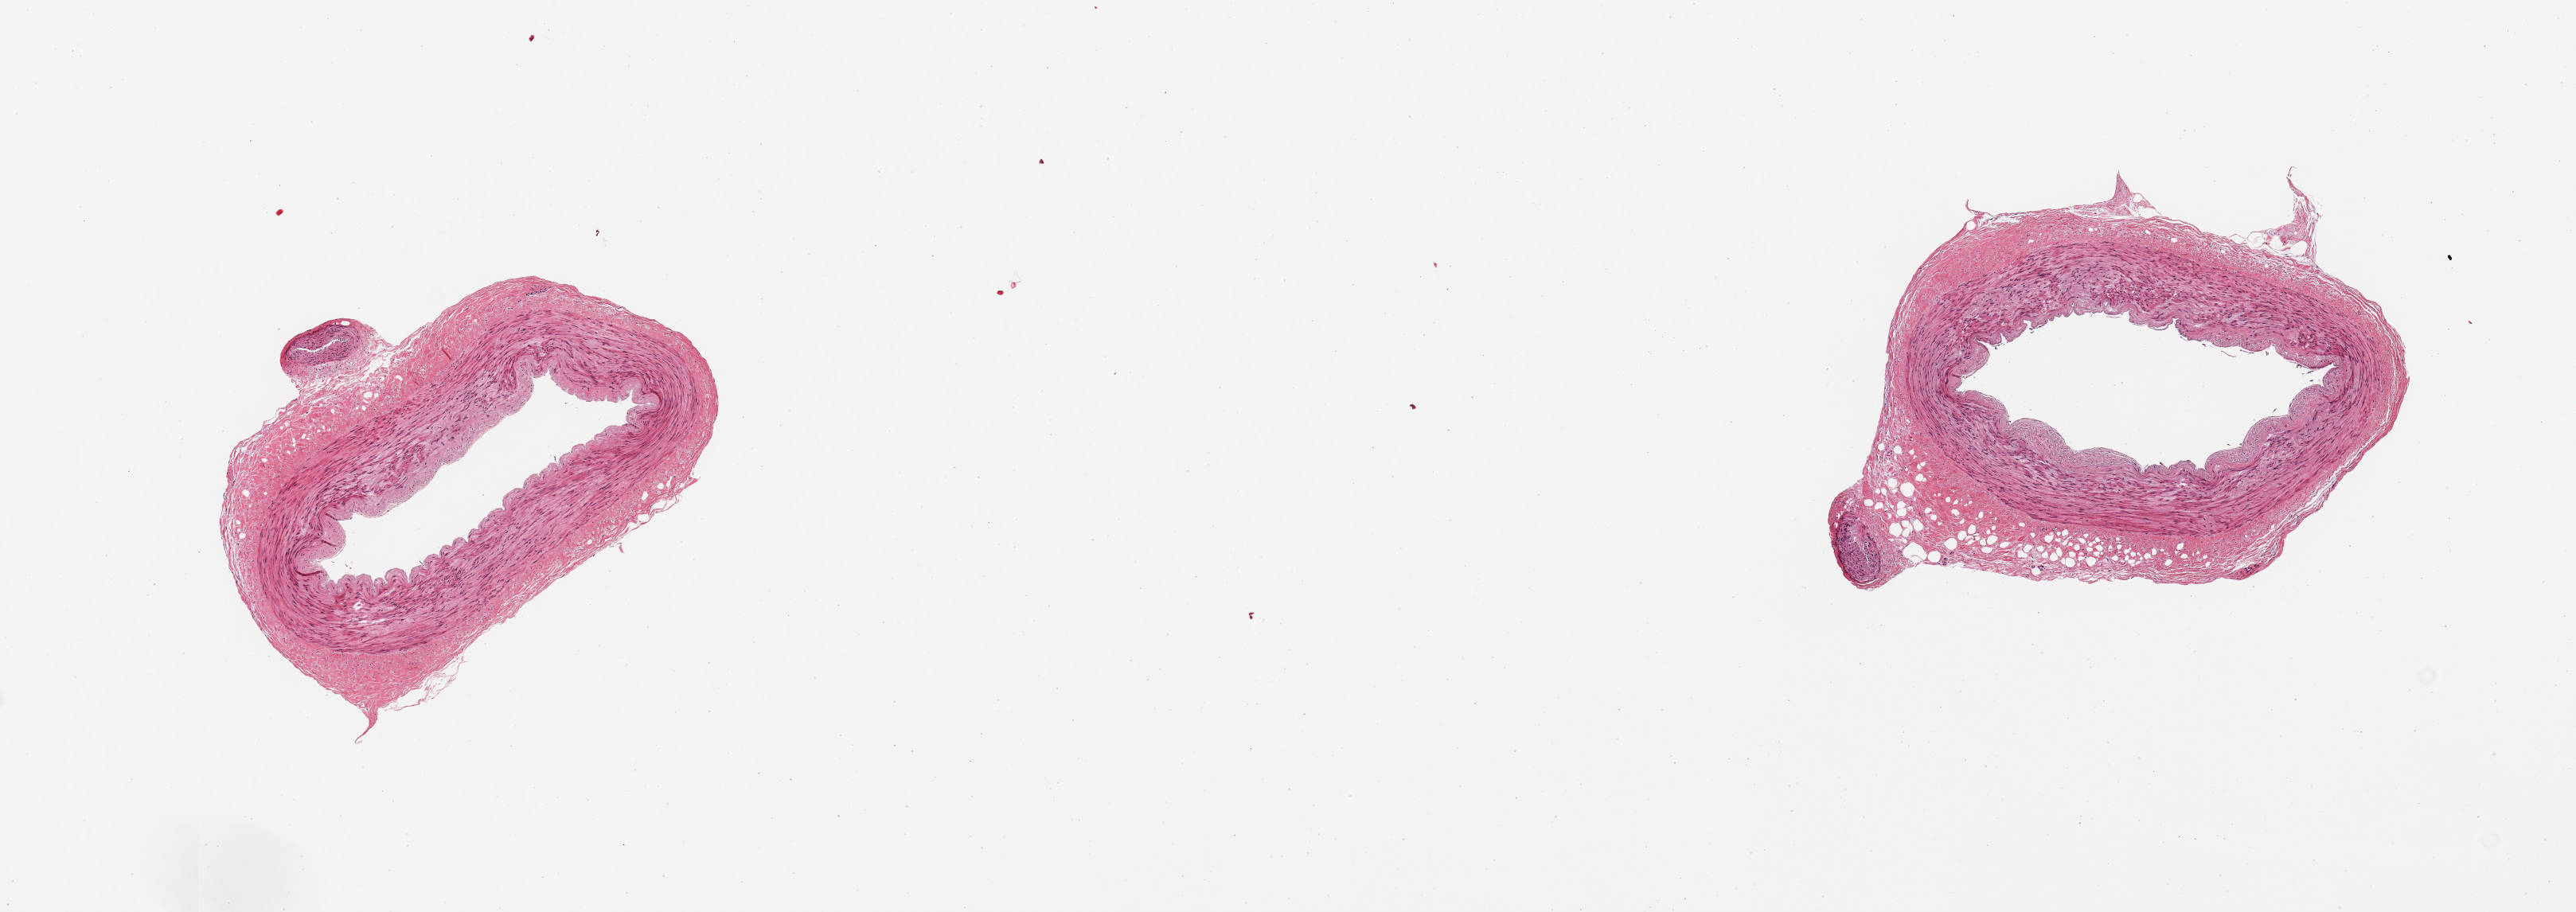
Hematoxylin and eosin (H&E) whole-slide image, brightfield — low-resolution overview of the scanned area, about 12.8 x 4.5 mm; PAXgene-fixed paraffin-embedded (PFPE) section; target tissue: tibial artery; tissue donor sample.
Reviewer comment on this tissue sample: 2 pieces; no lesions; 10% external fat.